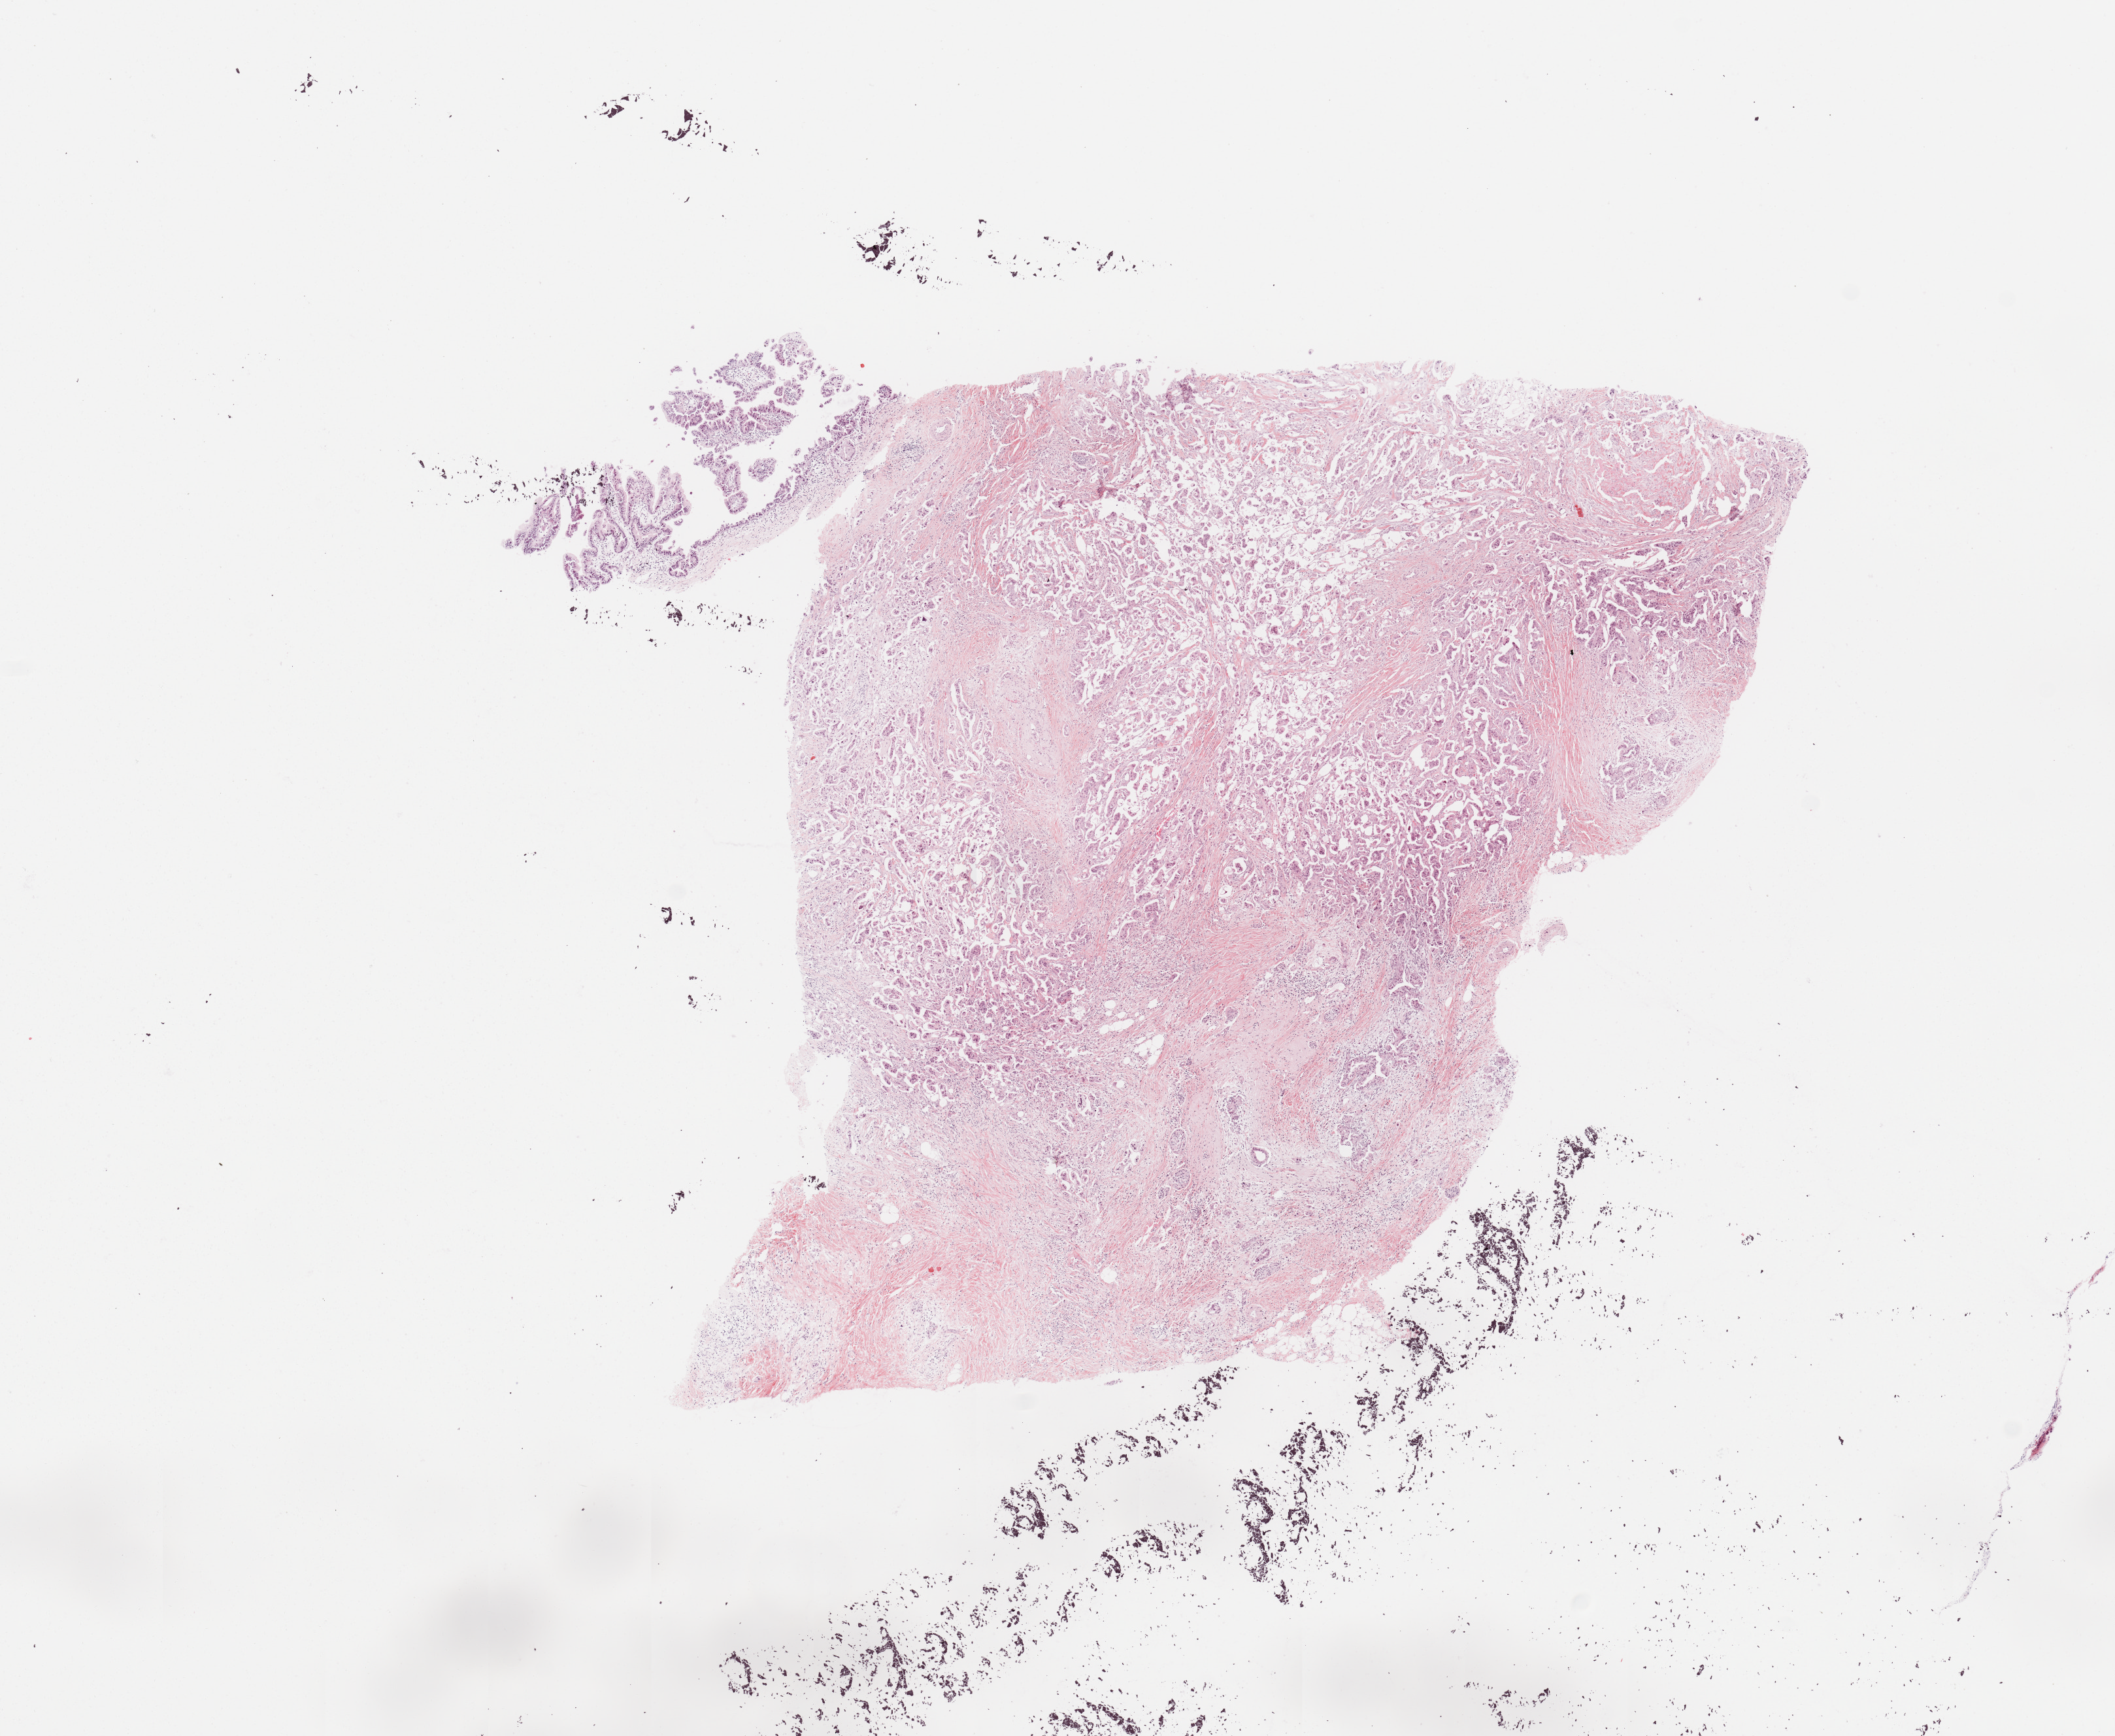
H&E-stained whole-slide image, whole scanned area (about 12.8 x 10.5 mm, from a 20x scan) shown as a low-resolution overview. Tumour tissue sample, sampled site: pancreas. 64-year-old male patient. Histologic grade: G2 (moderately differentiated). Composition of this section per pathologist review: tumour nuclei 80%, necrosis 5%.
- AJCC pathologic stage: III
- histologic diagnosis: Infiltrating duct carcinoma, NOS
- primary tumour site (as recorded): head